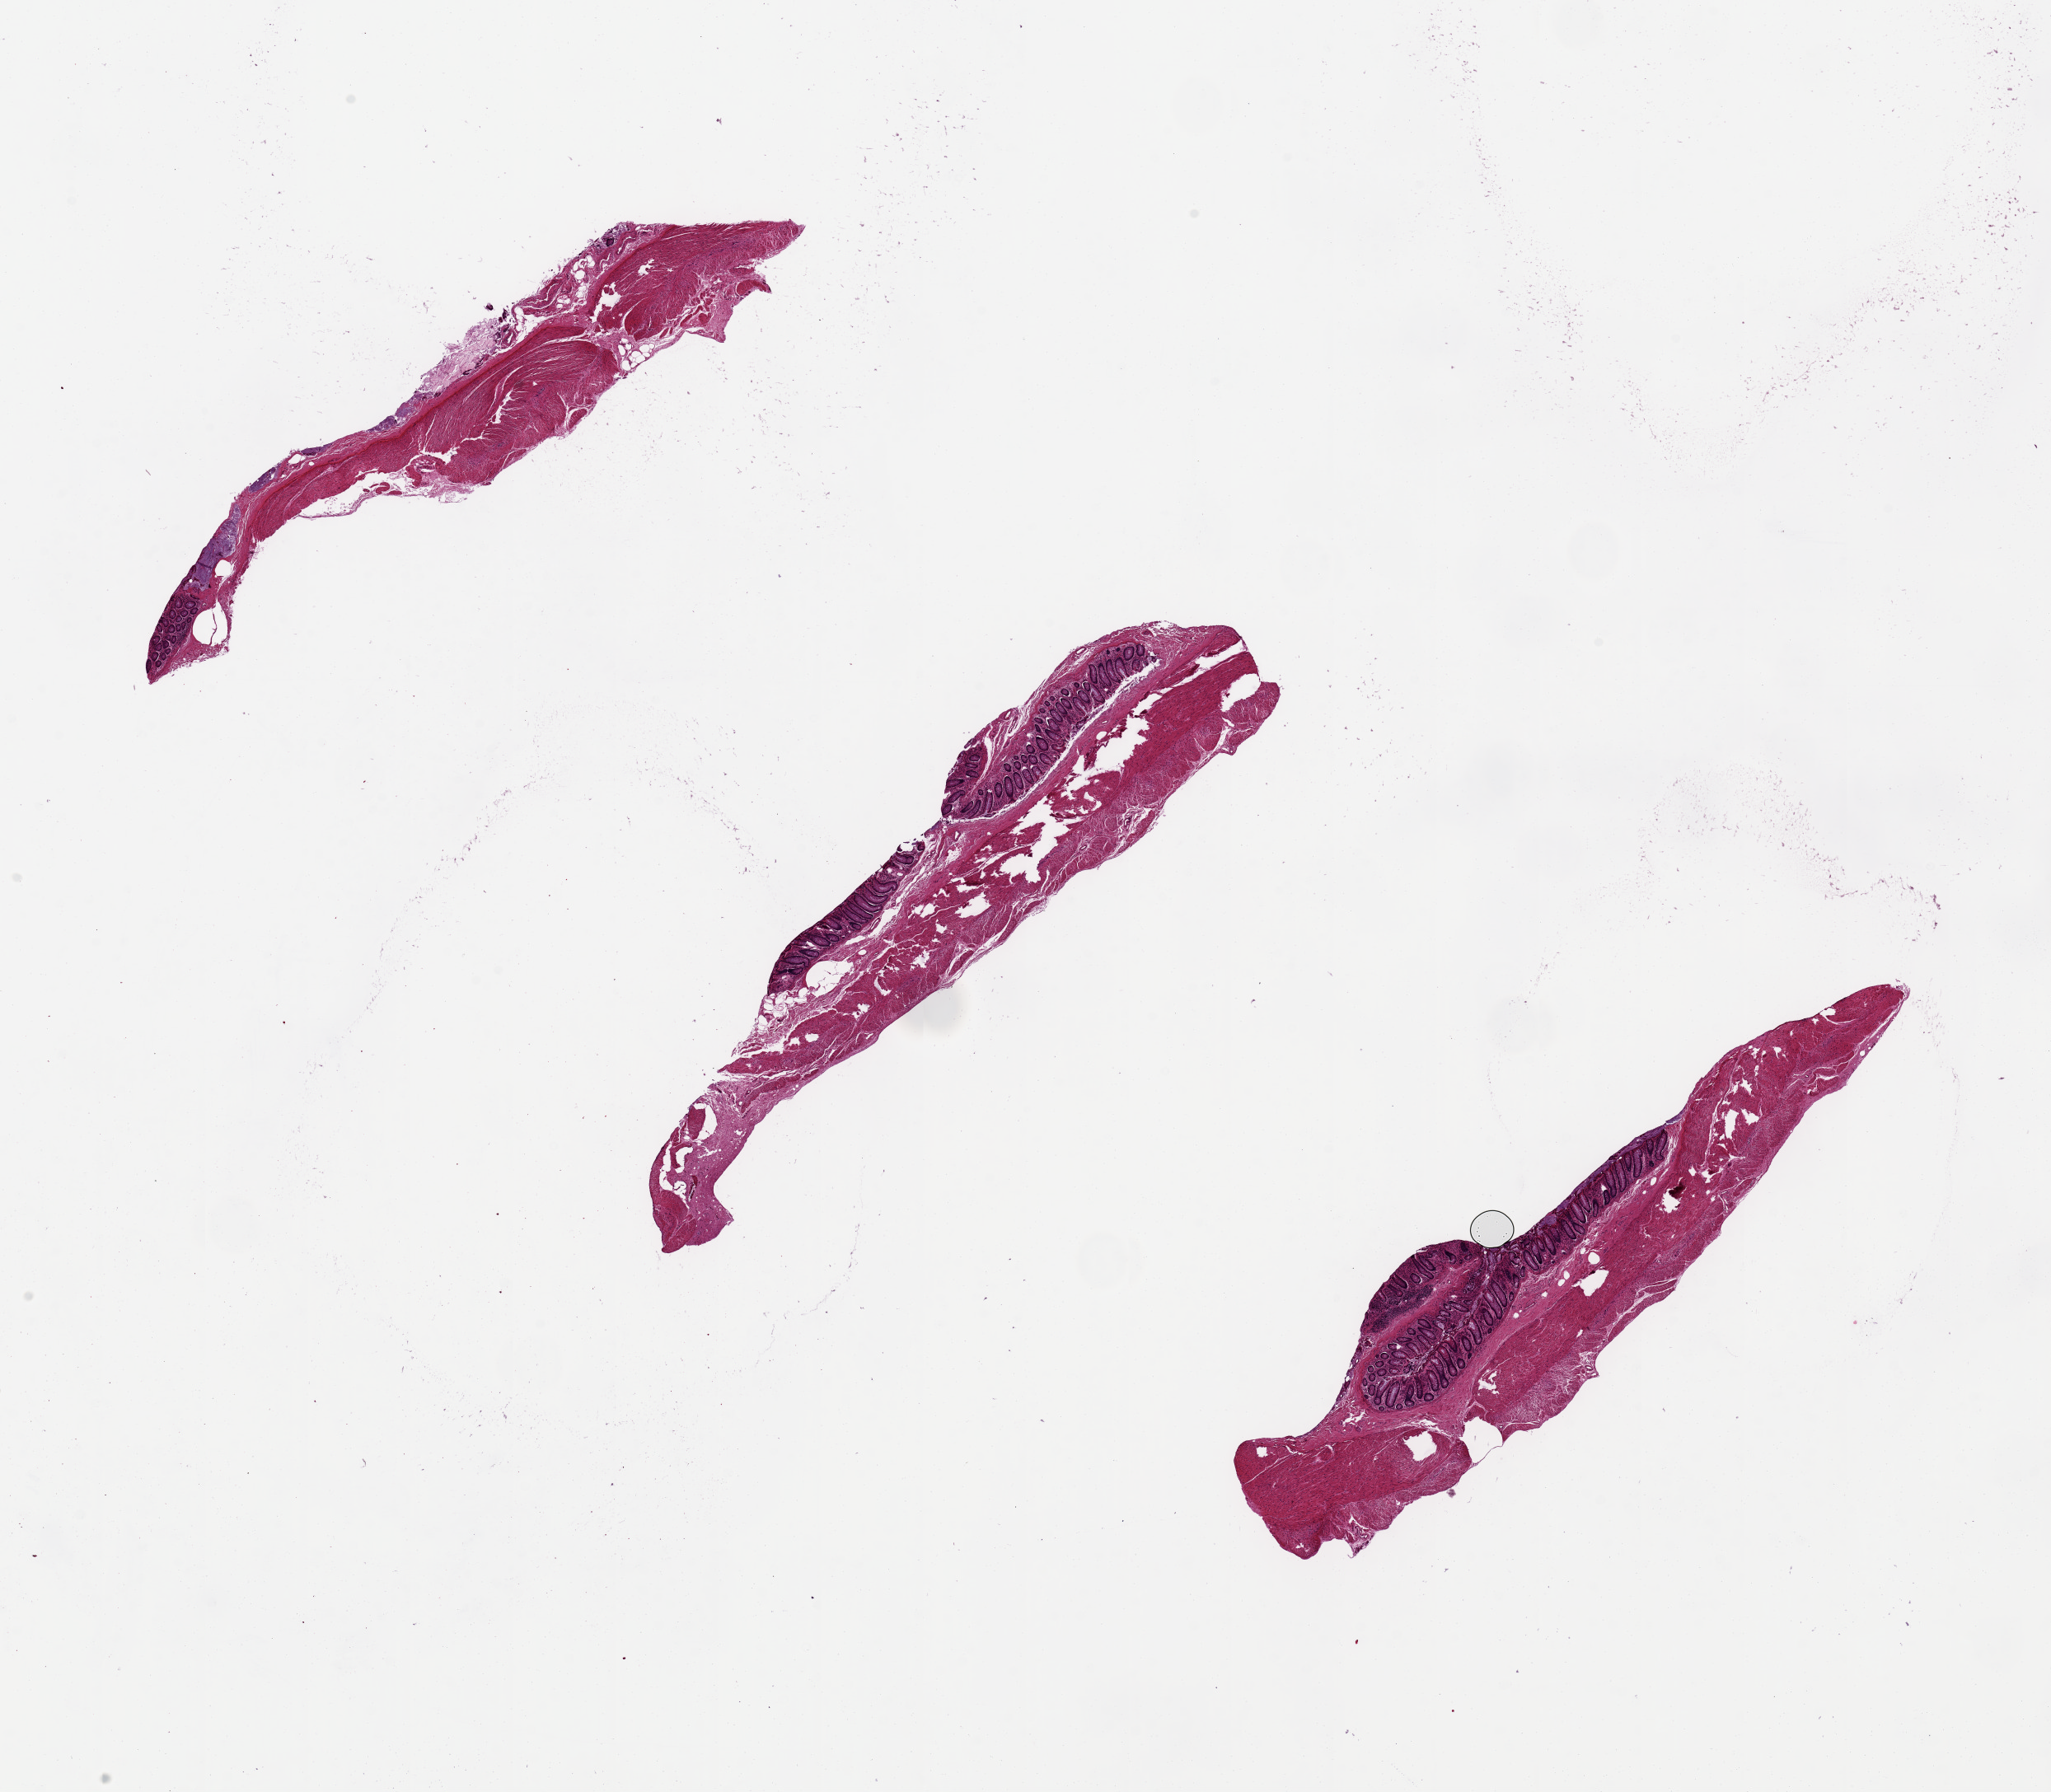
Digitized hematoxylin and eosin (H&E)-stained section — shown as a low-resolution overview of the whole scanned area (about 19.7 x 17.2 mm, slide scanned at 20x), PAXgene-fixed paraffin-embedded (PFPE) section, target tissue: transverse colon, donor tissue sample.
Review note (as recorded): 1 piece with minimal mucosa; 1 with abundant mucosa.